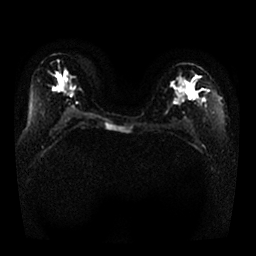
Breast MRI, one axial slice. Slice 16 of 25 in the series (ordered by position). Diffusion-weighted series; image 2 of 4 stored at this slice position (different b-values; order by instance number). 1.5 T. 256 × 256 image matrix, field of view 350 × 350 mm. Female patient.
Structures marked on this image (expert manual segmentation):
- tumour on diffusion-weighted imaging: bounding box (x1, y1, x2, y2) in pixels: (187, 88, 191, 96)